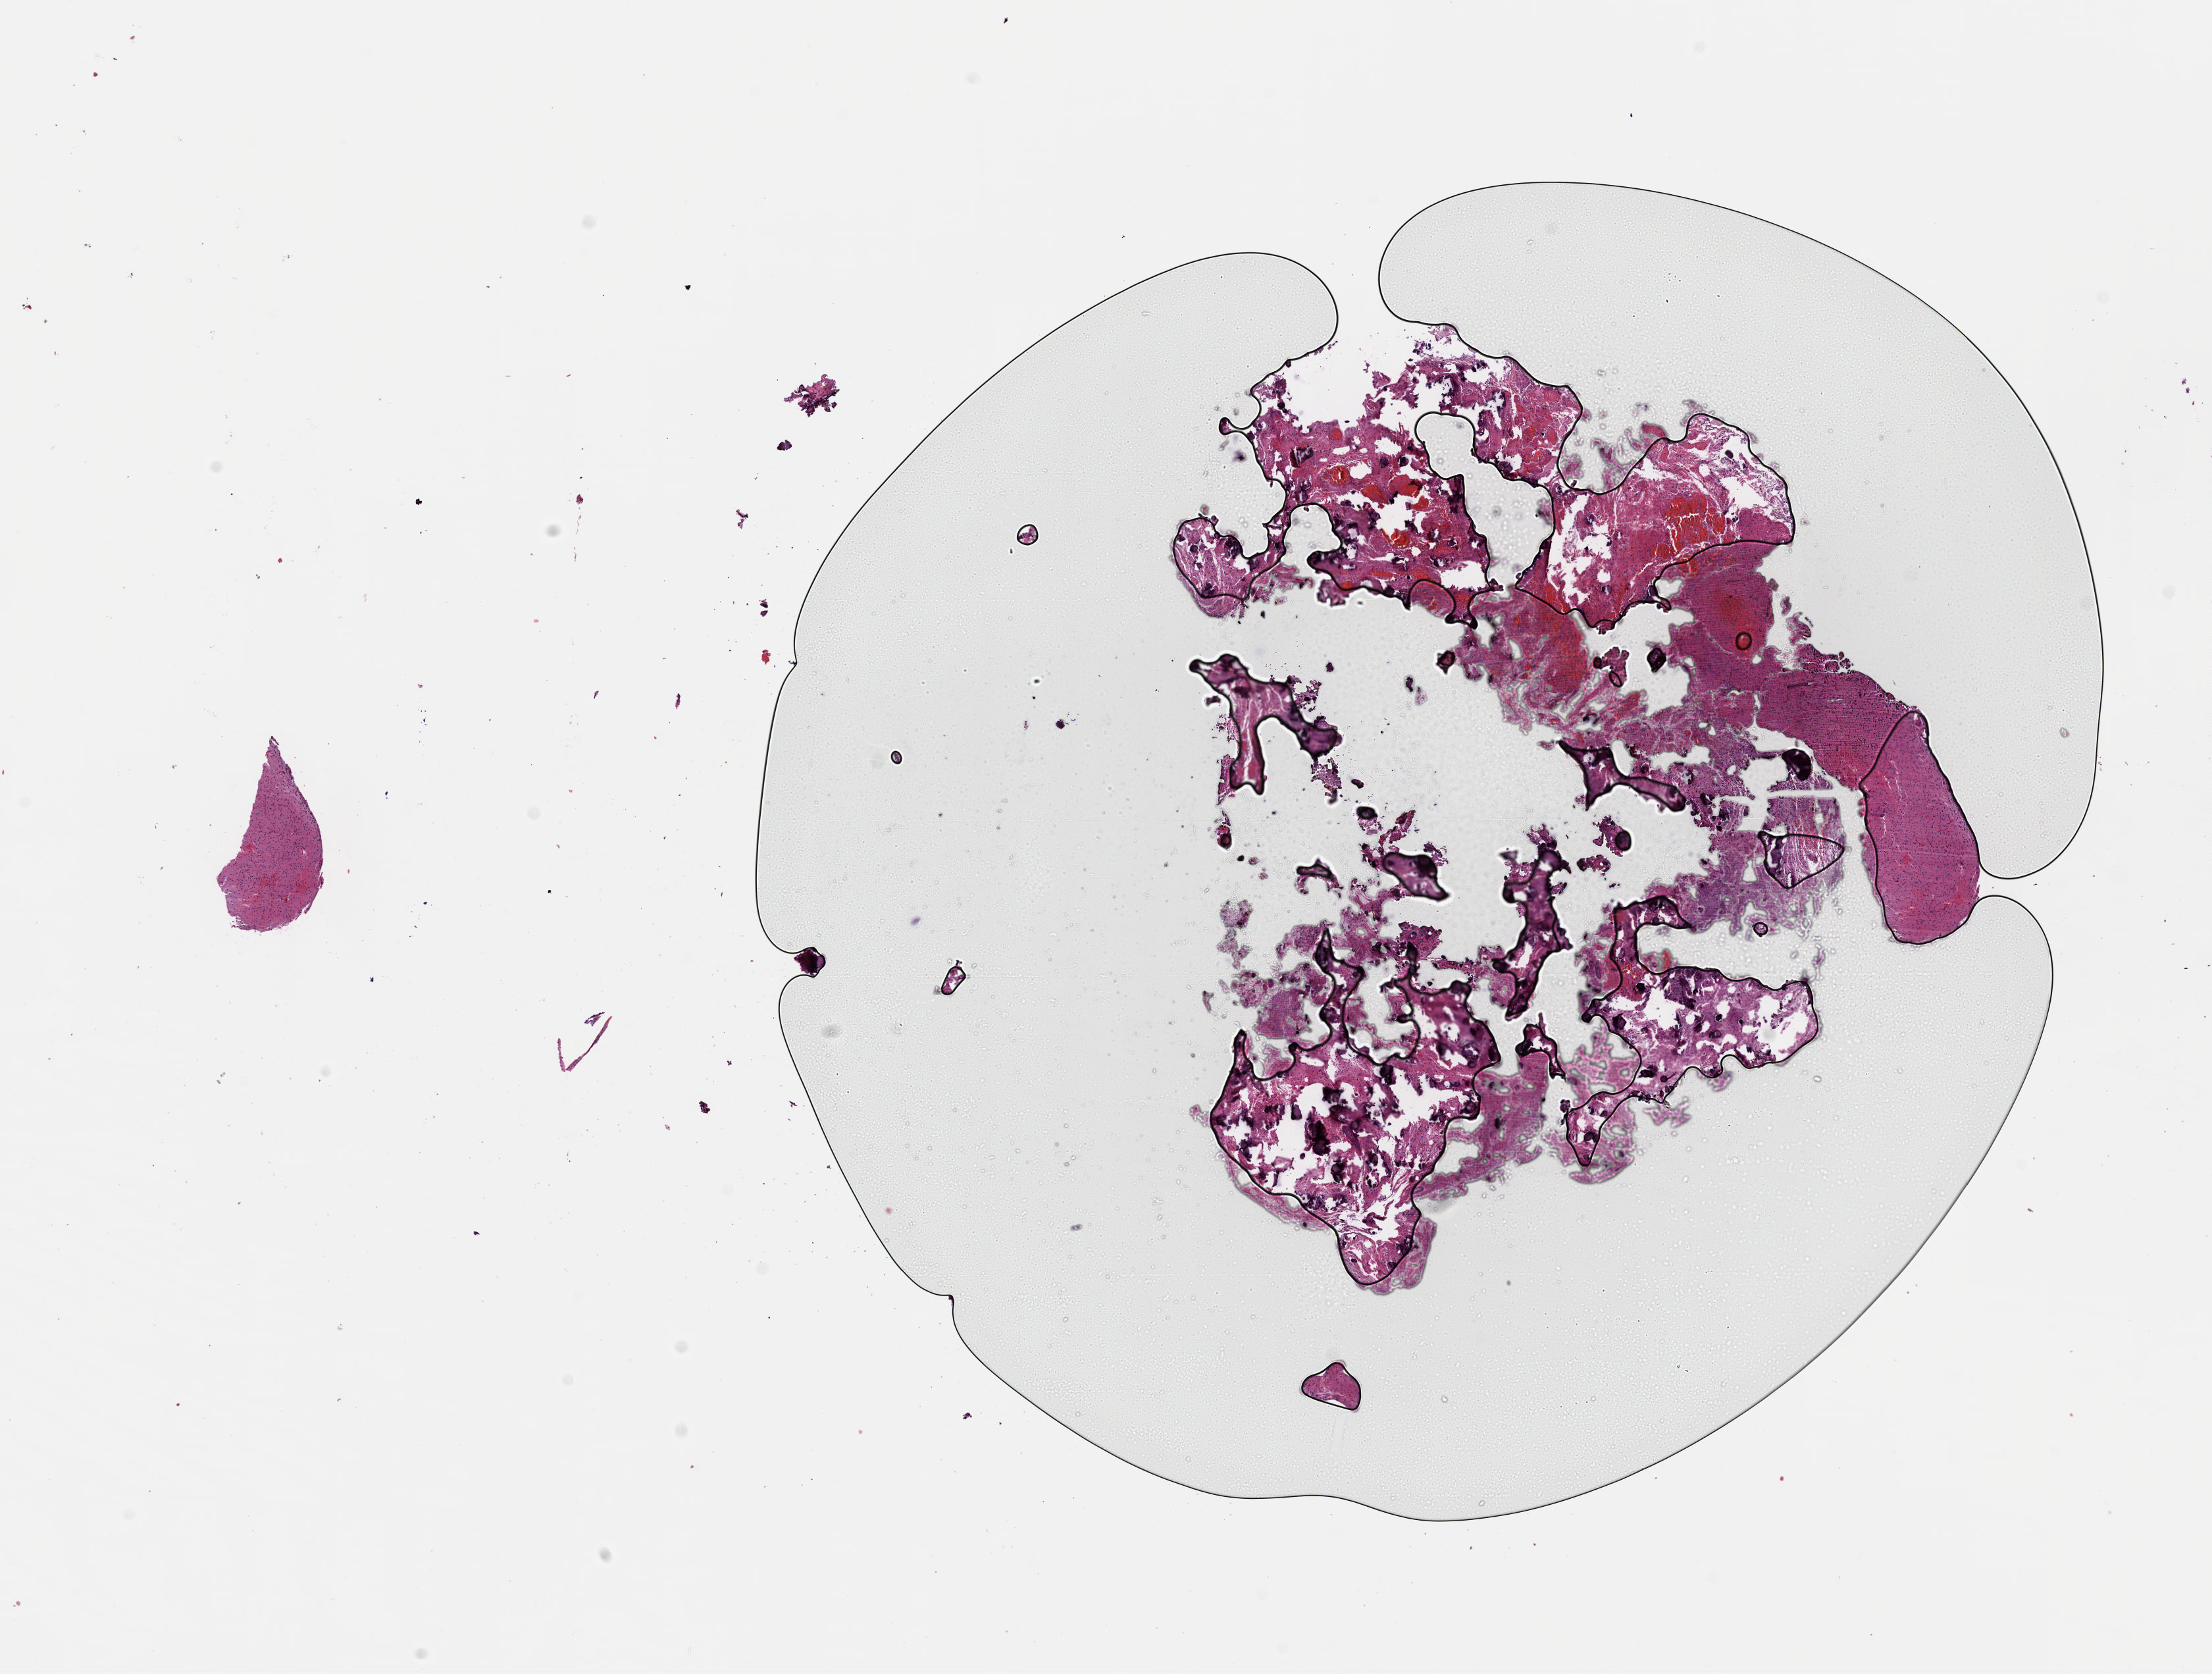
Digitized Hematoxylin and eosin (H&E) stained tissue section (whole slide) — shown as a low-resolution overview of the whole scanned area (about 13.6 x 10.3 mm, from a 40x scan), formalin-fixed paraffin-embedded (FFPE) diagnostic section, primary tumour sample from the brain. Female, age 31 years at initial diagnosis. Histologic grade: G2 (moderately differentiated).
• histologic diagnosis: Astrocytoma, NOS (cerebrum)